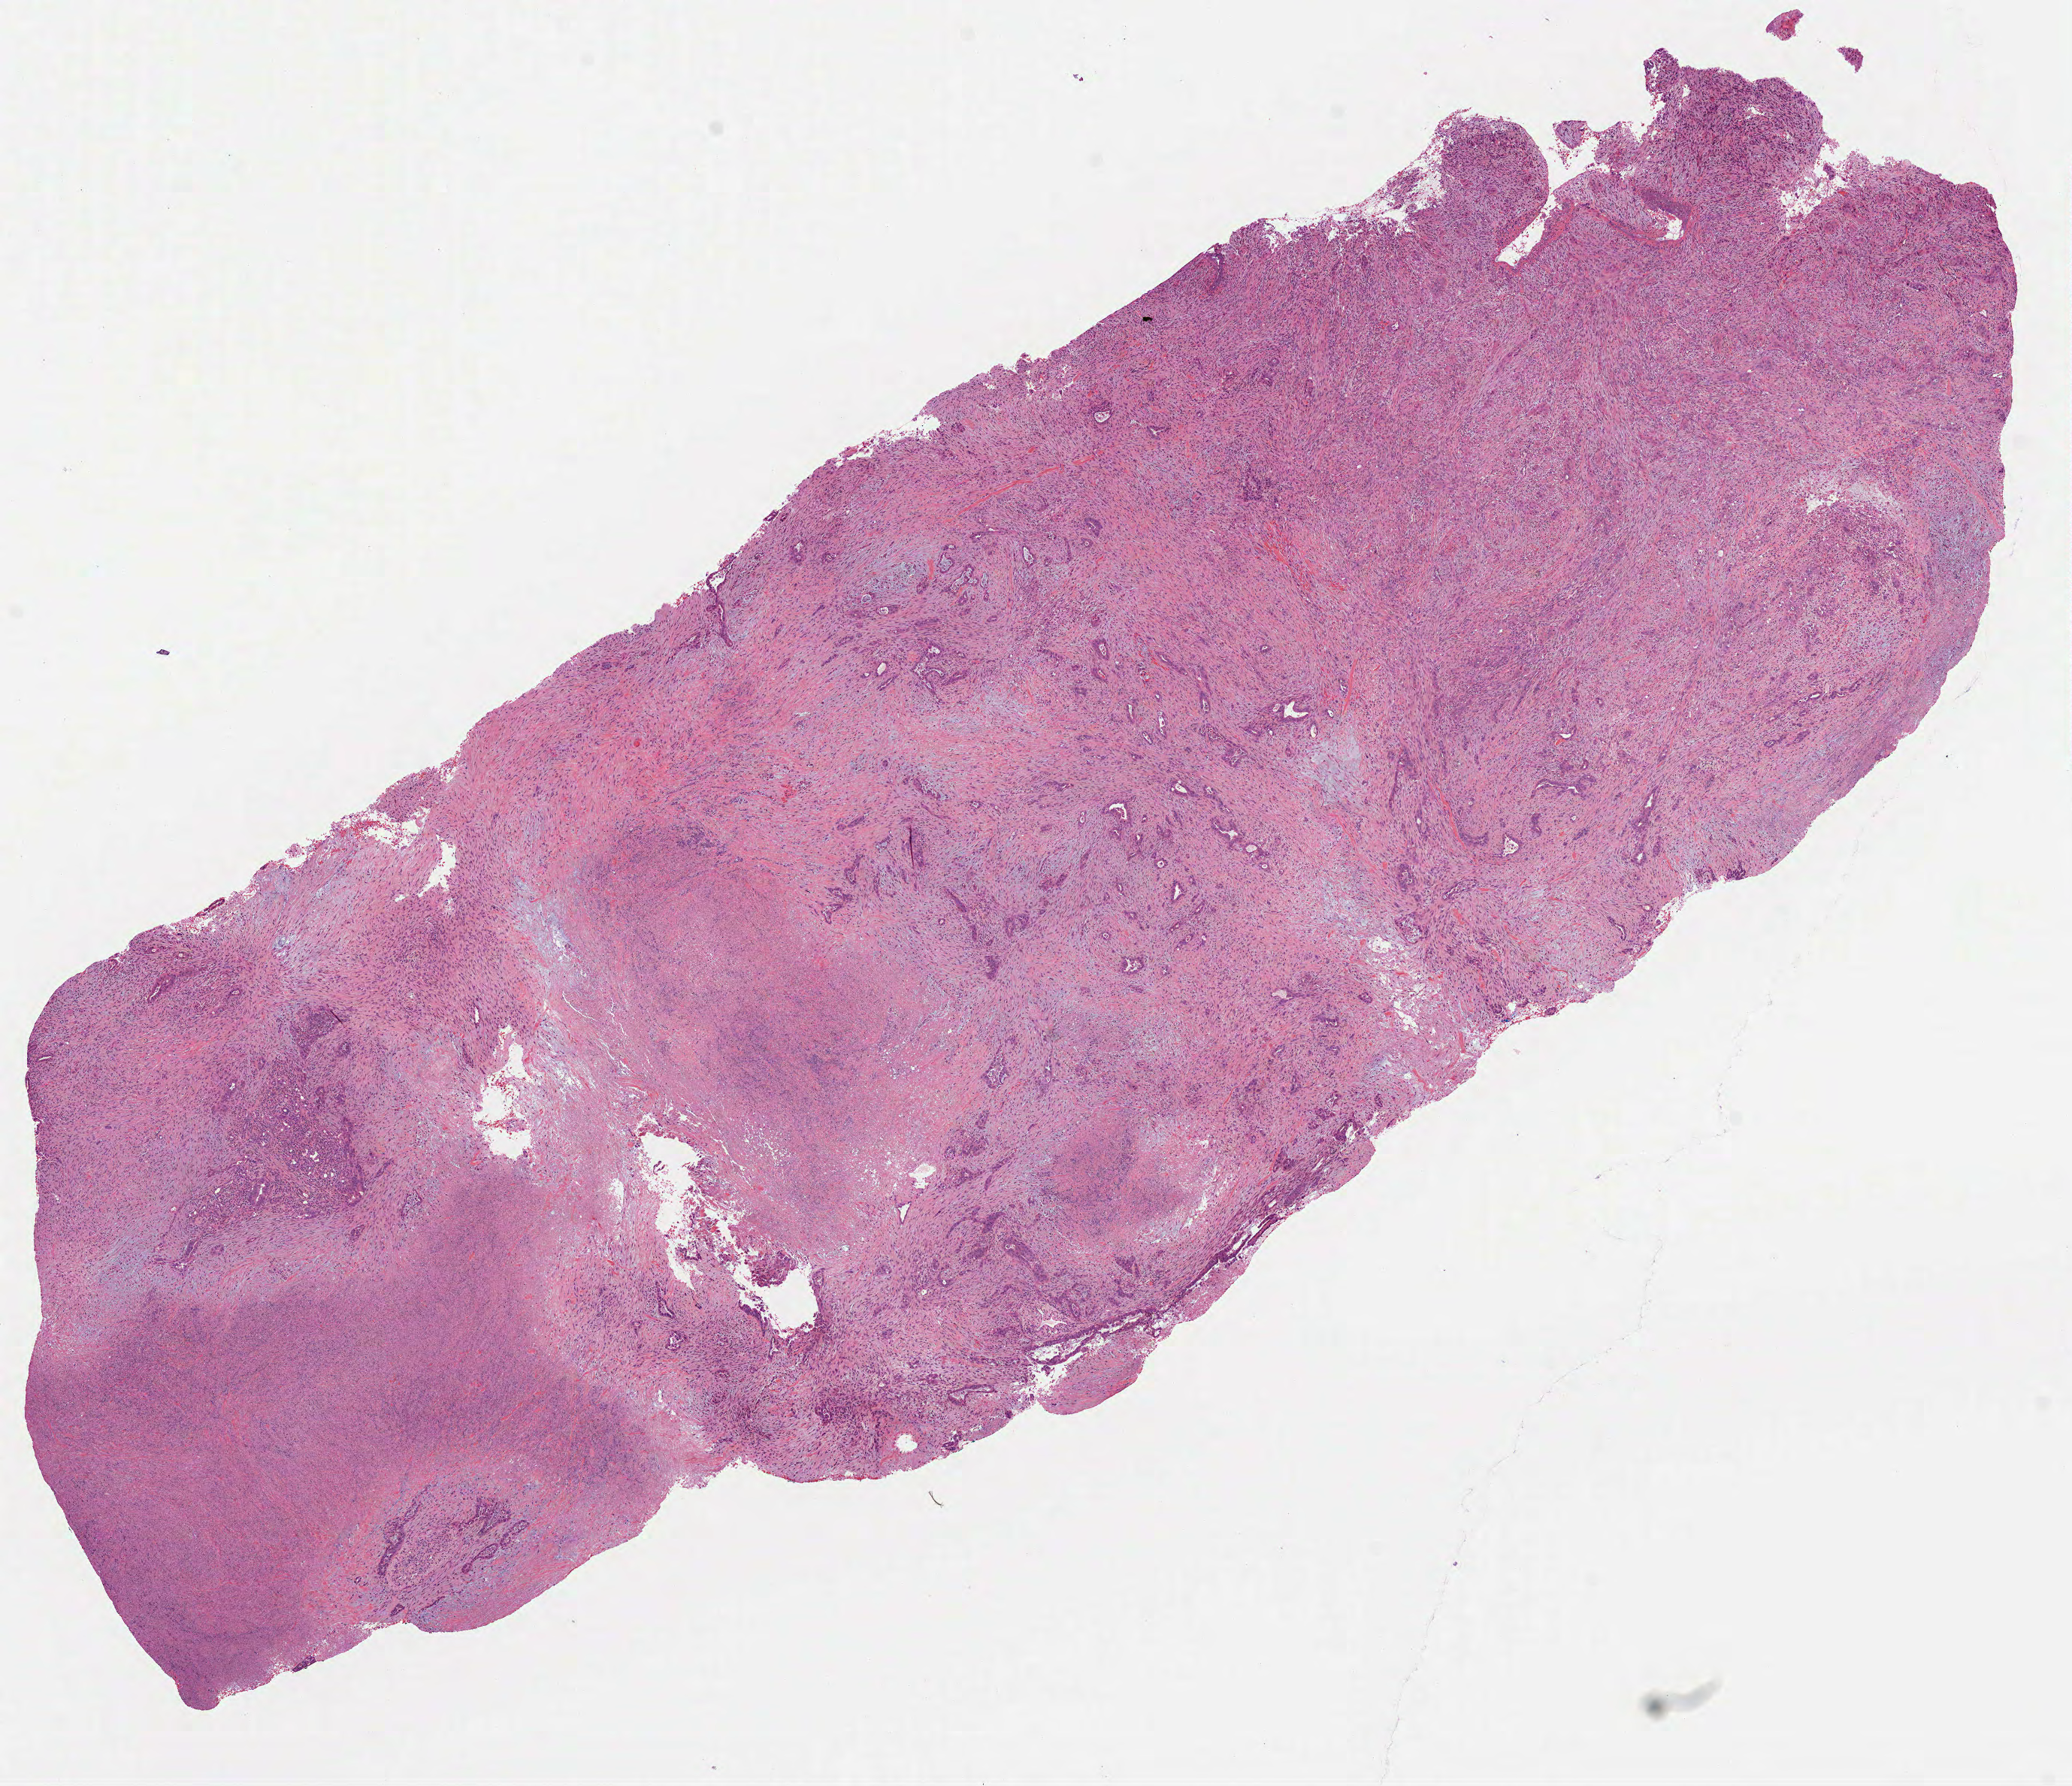
Digitized H&E-stained tissue section (whole slide) — low-resolution overview of the scanned area, about 11.1 x 9.6 mm (from a 40x scan), formalin-fixed paraffin-embedded (FFPE) diagnostic section, sample: primary tumour, pancreas. Patient: male, age at initial diagnosis 81 years. Histologic grade: G3 (poorly differentiated).
TNM: T3 N1 MX. Pathologic diagnosis: Infiltrating duct carcinoma, NOS. AJCC pathologic stage: IIB (7th edition).